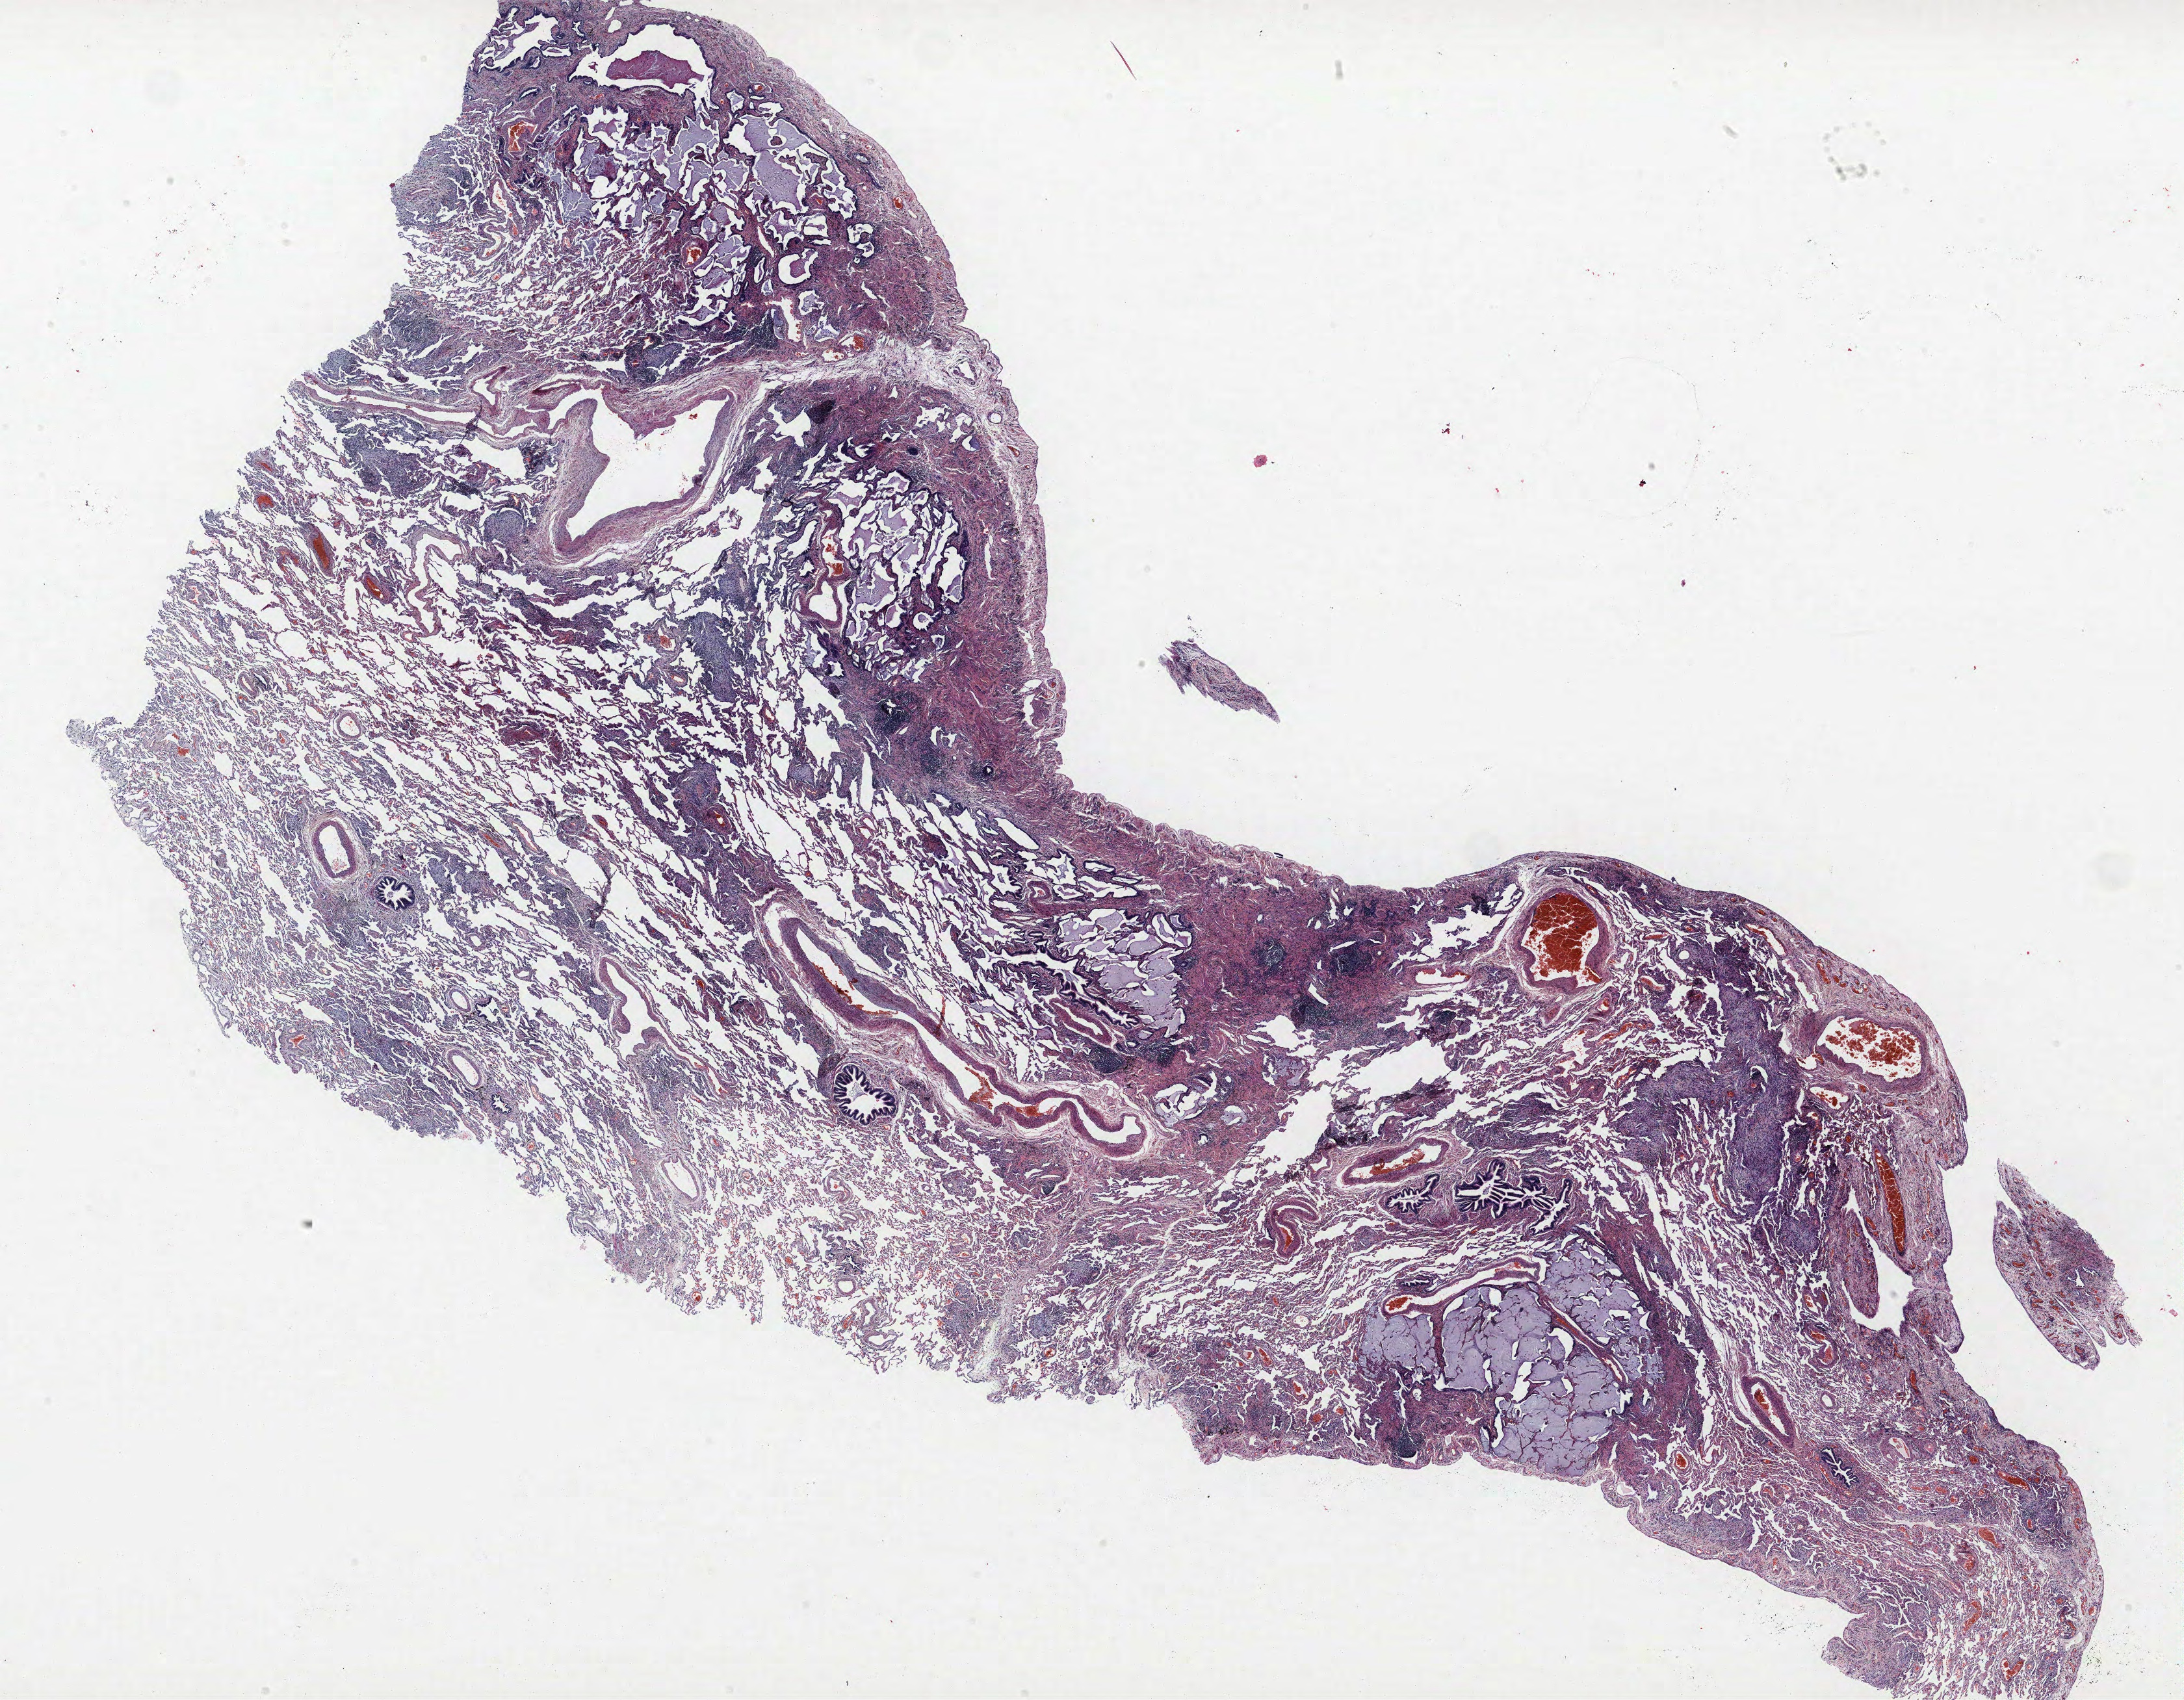
H&E-stained whole-slide image, whole scanned area (about 26.9 x 20.9 mm, acquisition: 40x scan) shown as a low-resolution overview, FFPE section, lung. Male, age 68 at enrolment. Current smoker at enrolment. Grade: moderately differentiated (G2).
- primary tumour location (clinical record): right lower lobe
- ICD-O-3 topography: lower lobe of lung (C34.3)
- participant's lung-cancer diagnosis: Adenosquamous carcinoma
- stage (AJCC 6th edition): IB
- tumour size (pathology): 40 mm